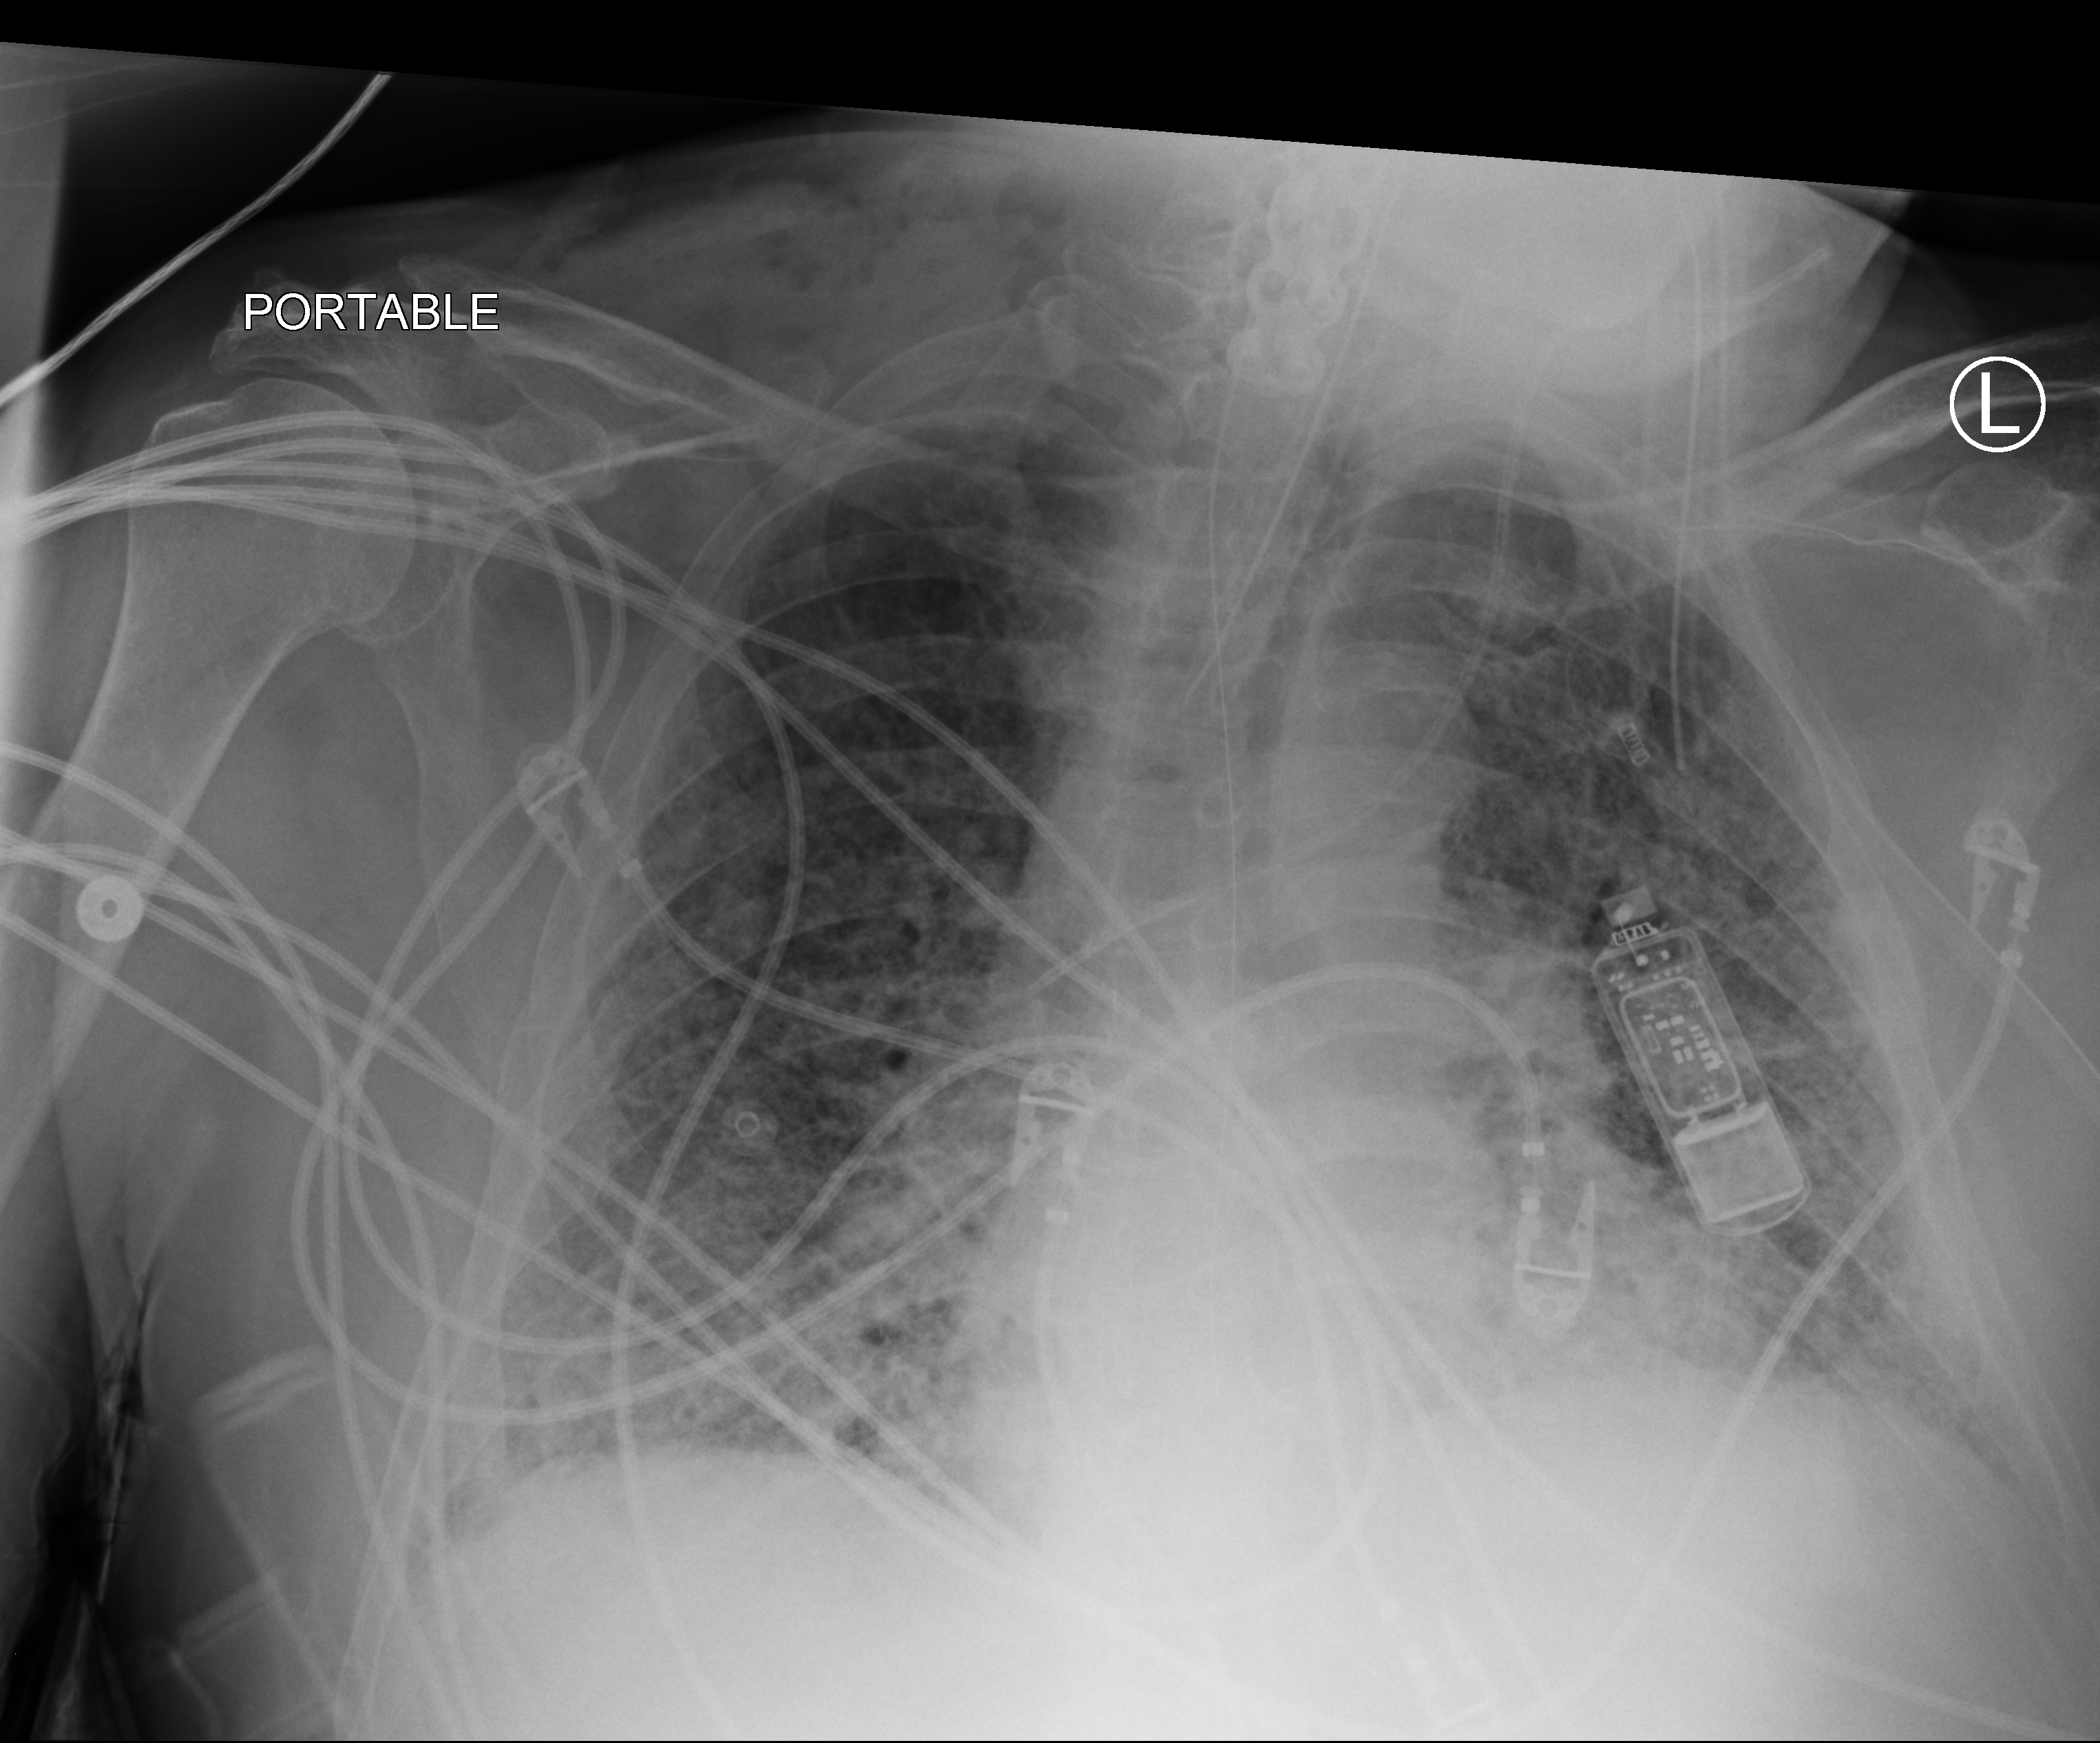
Chest X-ray (portable). Patient hospitalised with COVID-19; male, aged 60–74 years.
From the hospital-stay record, not from the radiograph (when in the stay this image was taken is not recorded):
- other chronic lung disease (admission record): yes
- mechanically ventilated during this hospital stay: yes
- length of hospital stay: 7 days